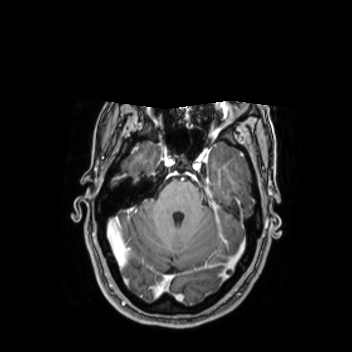
Brain MRI from a brain-tumour surgery series, one axial slice. Slice 177 of 350 in the series (ordered by position). T1-weighted post-contrast. 352 × 352 image matrix, field of view 280 × 280 mm. Case-level facts recorded for this patient, not image findings: histopathology: Oligodendroglioma; WHO grade: 2.
Outlined on this slice (outlined manually by an expert reader):
- tumour: bounding box [x1, y1, x2, y2] px = [227, 184, 234, 196]